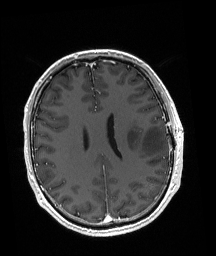
Brain MRI from a brain-tumour surgery series, one axial slice. Slice 75 of 192 in the series (ordered by position). T1-weighted post-contrast. 1 mm slice thickness. 216 × 256 image matrix, field of view 211 × 250 mm. Case-level facts recorded for this patient, not image findings: histopathology: Astrocytoma; WHO grade: 3; IDH mutation: yes.
Structures marked on this image (manually delineated by an expert):
- tumour: bounding box <127,126,166,155> (left, top, right, bottom; pixels)